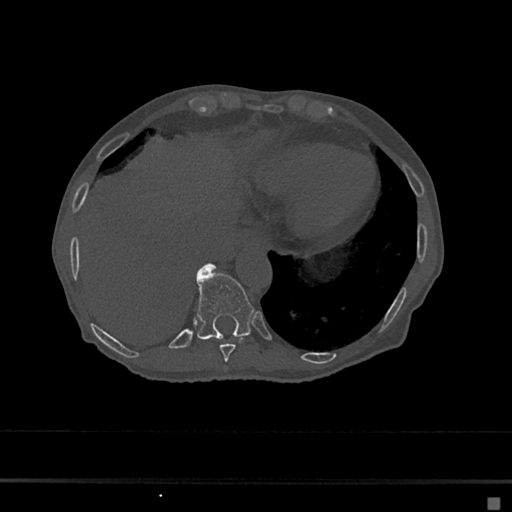
CT including the spine, one axial slice. Position 241 of 797 along the scan axis. Bone window (W 1800 / L 400 HU). 0.5 mm slice thickness. 512 × 512 image matrix, field of view 360 × 360 mm. Patient: female, 68 years. Case-level facts recorded for this patient, not image findings: primary cancer: renal.
Annotated regions visible in this slice (semi-automatically segmented with operator editing):
- T10 vertebra: bounding box [x1, y1, x2, y2] px = [197, 264, 254, 340]
- T11 vertebra: [200, 267, 203, 270]
- T9 vertebra: [219, 338, 244, 362]